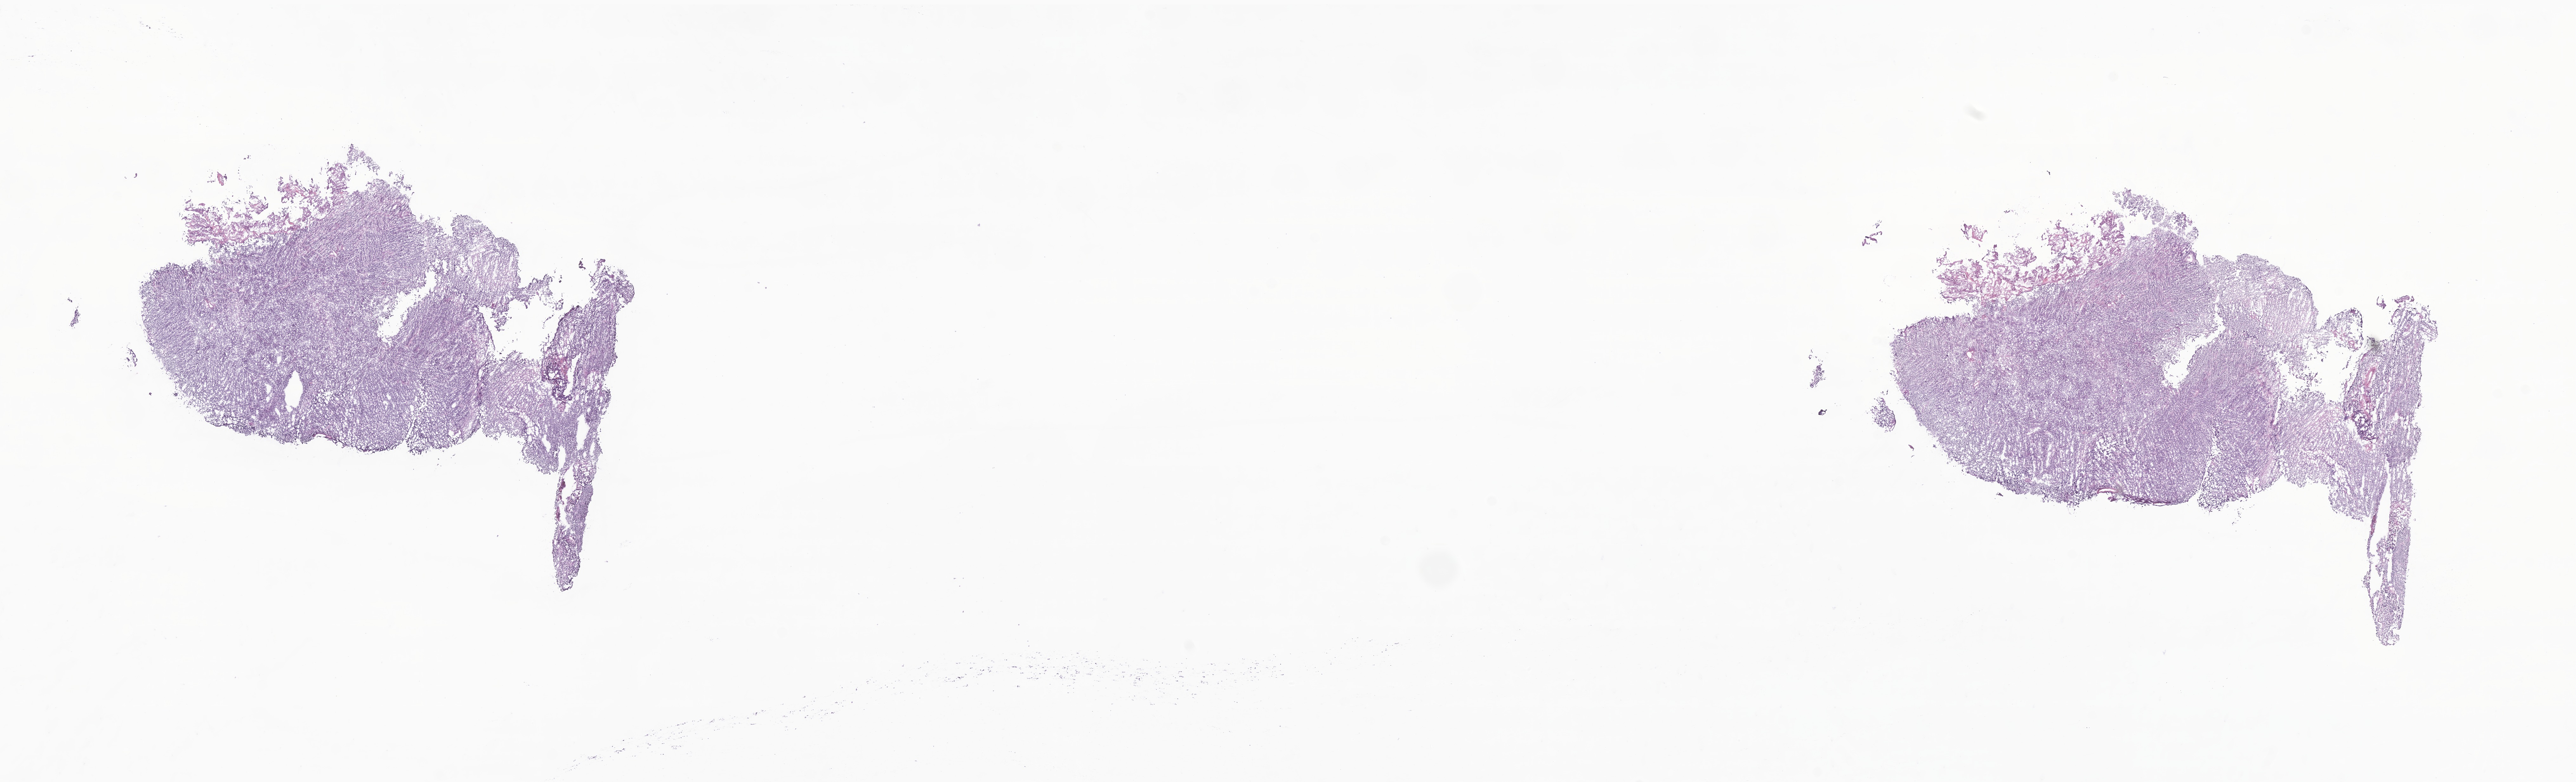
Hematoxylin and eosin (H&E) whole-slide image of tumor tissue from the cerebellum — whole scanned area (about 34.2 x 10.4 mm) shown as a low-resolution overview, frozen section (OCT-embedded). Male patient, age 149 months (12 years 5 months).
* diagnosis (ICD-O-3 morphology term): Desmoplastic nodular medulloblastoma